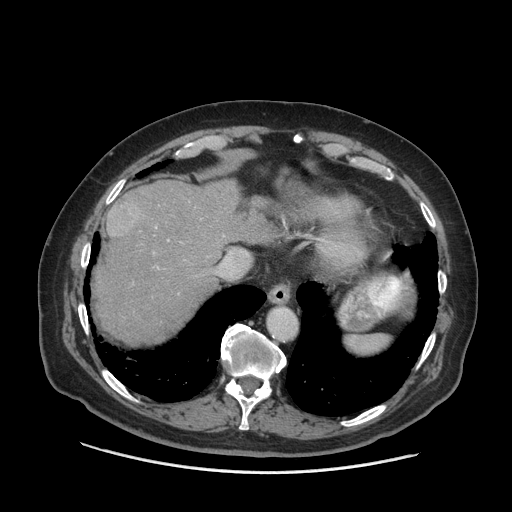
Contrast-enhanced abdominal CT (liver protocol), one axial slice; slice 58 of 77 in the series (ordered by position); reconstruction kernel STANDARD; soft-tissue window (W 400 / L 40 HU); 2.5 mm slice thickness; 512 × 512 image matrix, field of view 420 × 420 mm. Case-level facts recorded for this patient, not image findings: diagnosis: hepatocellular carcinoma (patient treated with transarterial chemoembolisation; whether this scan precedes or follows treatment is not stated here); TNM stage (as recorded): Stage-I; Child-Pugh class: A; tumour differentiation: well differentiated; tumour nodularity: uninodular.
Outlined on this slice (semi-automatically segmented with operator editing):
- abdominal aorta: box from (x=269, y=308) to (x=297, y=339) px
- liver parenchyma outside the tumour (the mass and vessels are separate outlines, so this box may not span the whole liver): (x=94, y=180)–(x=274, y=342)
- mass: (x=106, y=203)–(x=143, y=238)